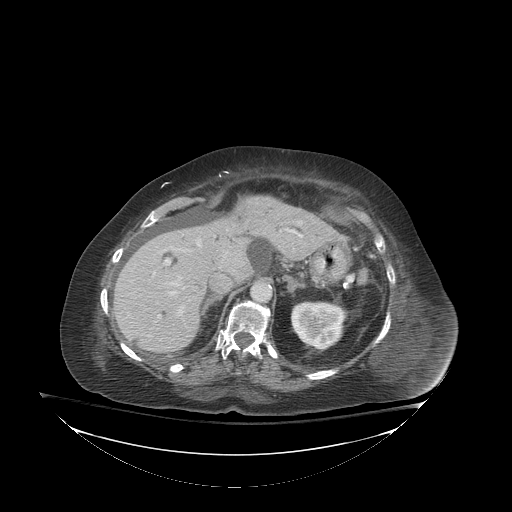
Contrast-enhanced abdominal CT (liver protocol), one axial slice. Position 57 of 81 along the scan axis. 140 kVp. Soft-tissue window (W 400 / L 40 HU). 512 × 512 image matrix. From the clinical record (not read from this slice): diagnosis: hepatocellular carcinoma (patient treated with transarterial chemoembolisation; whether this scan precedes or follows treatment is not stated here); TNM stage (as recorded): Stage-I; Child-Pugh class: B; tumour differentiation: well-moderately differentiated; tumour nodularity: uninodular.
Structures marked on this image (semi-automatically segmented with operator editing):
- liver parenchyma outside the tumour (the mass and vessels are separate outlines, so this box may not span the whole liver): box from (x=114, y=196) to (x=336, y=352) px
- mass: (x=233, y=205)–(x=248, y=222)
- liver vessels: (x=165, y=229)–(x=302, y=315)